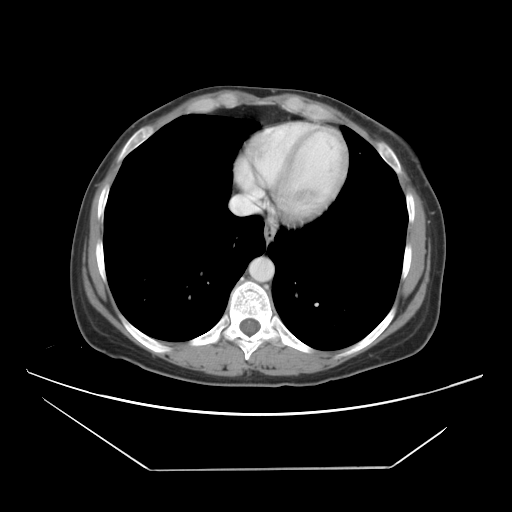
Contrast-enhanced abdominal CT, one axial slice; position 40 of 42 along the scan axis; intravenous contrast given; soft-tissue window (W 400 / L 40 HU); 5 mm slice thickness; 512 × 512 image matrix. Female patient, age 52 years. Case-level facts recorded for this patient, not image findings: diagnosis: colorectal cancer liver metastases, imaged before liver resection; multiple liver metastases: yes; largest metastasis: 5.5 cm; disease in both lobes: yes.
Outlined on this slice (outlined manually by an expert reader):
- hepatic veins: bounding box <231,127,288,214> (left, top, right, bottom; pixels)